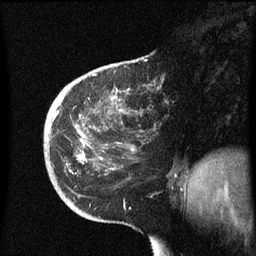
Breast MRI (dynamic contrast-enhanced), one sagittal slice. Position 20 of 60 along the scan axis. Dynamic contrast-enhanced series, image 2 of 3 at this slice position (ordered by acquisition). 1.5 T. TE 4.2 ms, TR 8.4 ms. 2.3 mm slice thickness. 256 × 256 image matrix. Female patient, age 38 years. Case-level facts recorded for this patient, not image findings: setting: breast cancer imaged before/during neoadjuvant chemotherapy; receptor status: HER2-positive.
Structures marked on this image (semi-automatically segmented with operator editing):
- analysis volume of interest (the breast-tissue region the enhancement analysis was run in; not a lesion): bounding box [x1, y1, x2, y2] px = [44, 78, 191, 213]
- tumour enhancement mask (voxels above the 70 % enhancement threshold inside the analysis volume of interest): [54, 112, 85, 161]